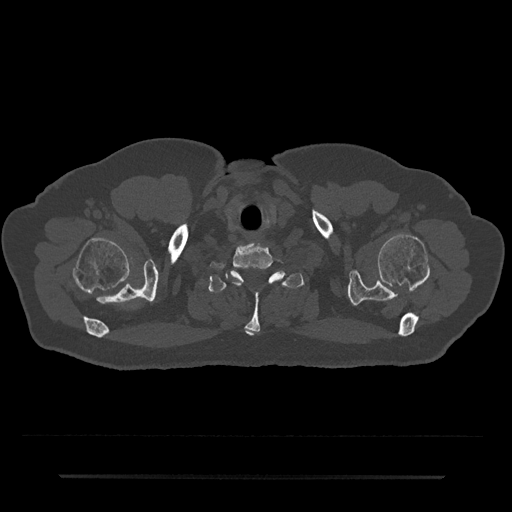
CT including the spine, one axial slice. Slice 657 of 797 in the series (ordered by position). Reconstruction kernel Br40s/3. Bone window (W 1800 / L 400 HU). 0.5 mm slice thickness. 512 × 512 image matrix, field of view 437 × 437 mm. Male patient, age 69 years. Case-level facts recorded for this patient, not image findings: primary cancer: prostate.
Structures marked on this image (semi-automatic segmentation, software-assisted and operator-edited):
- T1 vertebra: bounding box [x1, y1, x2, y2] px = [208, 271, 304, 336]